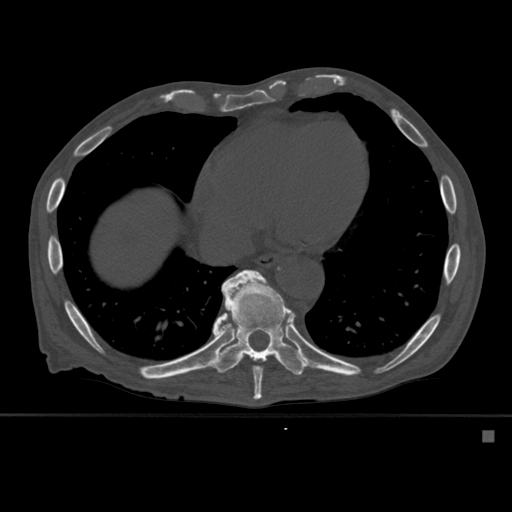
CT including the spine, one axial slice; position 322 of 527 along the scan axis; bone window (W 1800 / L 400 HU); 1.5 mm slice thickness; 512 × 512 image matrix, field of view 373 × 373 mm. Male patient, age 78 years. From the clinical record (not read from this slice): primary cancer: prostate.
Annotated regions visible in this slice (semi-automatically segmented with operator editing):
- T10 vertebra: bounding box [x1, y1, x2, y2] px = [212, 275, 307, 376]
- T9 vertebra: [222, 270, 293, 400]